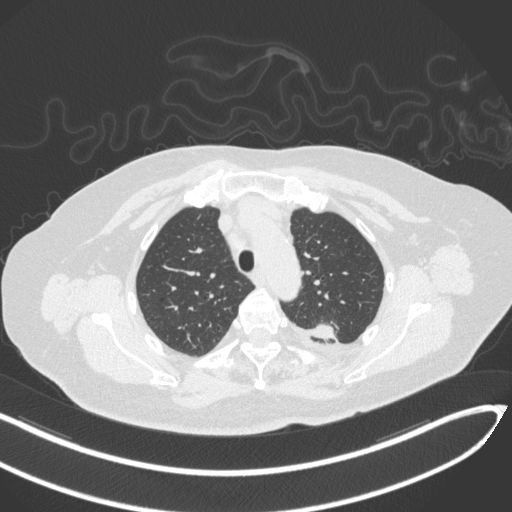
Chest CT, one axial slice; slice 249 of 270 in the series (ordered by position); lung window (W 1500 / L -600 HU); 1 mm slice thickness; 512 × 512 image matrix, field of view 400 × 400 mm. Female patient, age 76 years. Case-level facts recorded for this patient, not image findings: clinical TNM (as recorded): T1c N0 M0.
Structures marked on this image (rectangle marked by the reading radiologist):
- lung tumour (recorded histology: adenocarcinoma): bounding box [x1, y1, x2, y2] px = [308, 320, 337, 345]